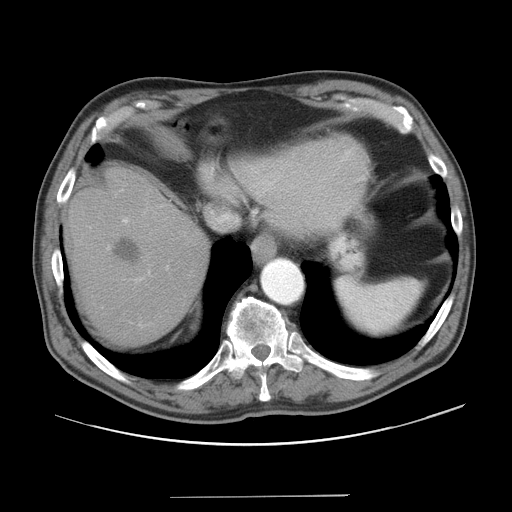
Contrast-enhanced abdominal CT, one axial slice. Position 35 of 41 along the scan axis. Reconstruction kernel STANDARD. 120 kVp. Intravenous contrast given. Soft-tissue window (W 400 / L 40 HU). 5 mm slice thickness. 512 × 512 image matrix, field of view 420 × 420 mm. Male patient, age 75 years. From the clinical record (not read from this slice): diagnosis: colorectal cancer liver metastases, imaged before liver resection; multiple liver metastases: no; largest metastasis: 5.2 cm; disease in both lobes: no.
Structures marked on this image (expert manual segmentation):
- hepatic veins: bounding box (x1, y1, x2, y2) in pixels: (210, 211, 236, 225)
- liver: (71, 168, 207, 343)
- planned liver remnant (the part of the liver to remain after resection): (99, 222, 207, 343)
- portal vein (with intrahepatic branches): (122, 218, 150, 273)
- liver metastasis: (114, 239, 141, 262)